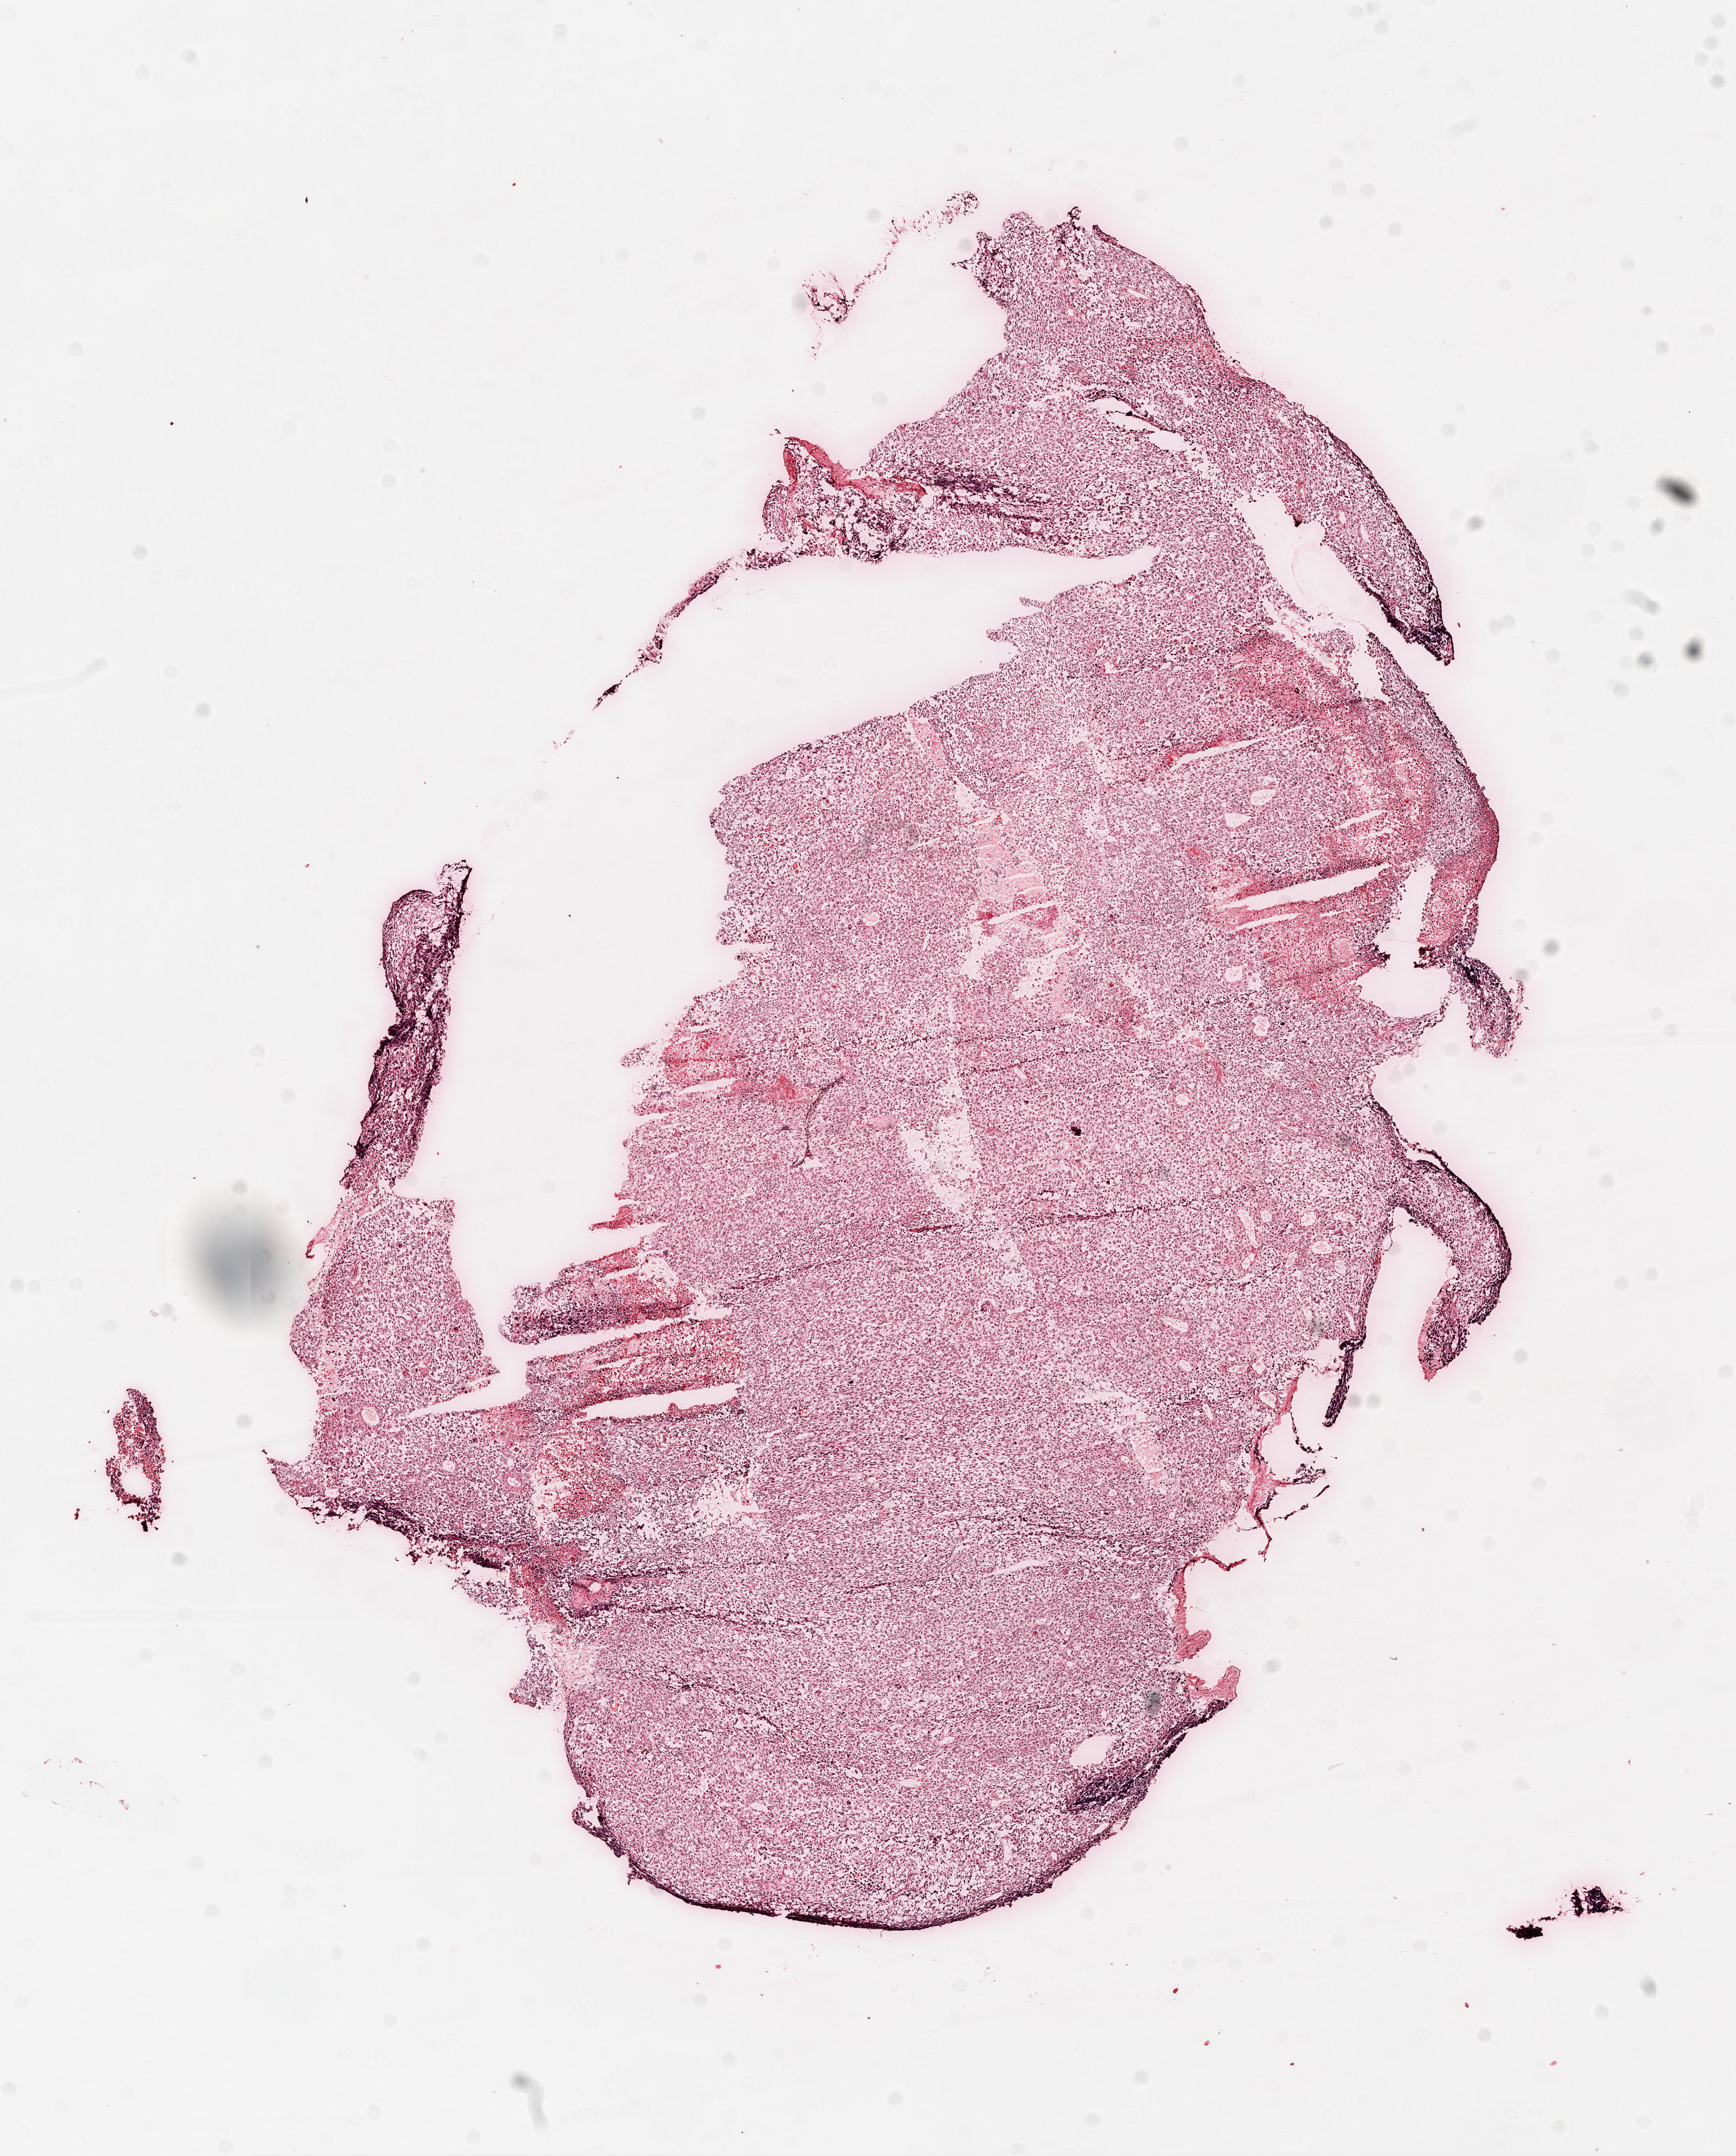
Whole-slide histology image, Hematoxylin and eosin (H&E) stained, a low-resolution overview of the entire scanned area, about 10.2 x 12.6 mm (acquisition: 20x scan), frozen section, sample: primary tumour, brain. Patient: female, age at initial diagnosis 74 years. Pathologist review of this section (percent, as recorded): tumour cells 95%, tumour nuclei 100%, normal cells 0%, stromal cells 0%, necrosis 5%.
Pathologic diagnosis: Glioblastoma.